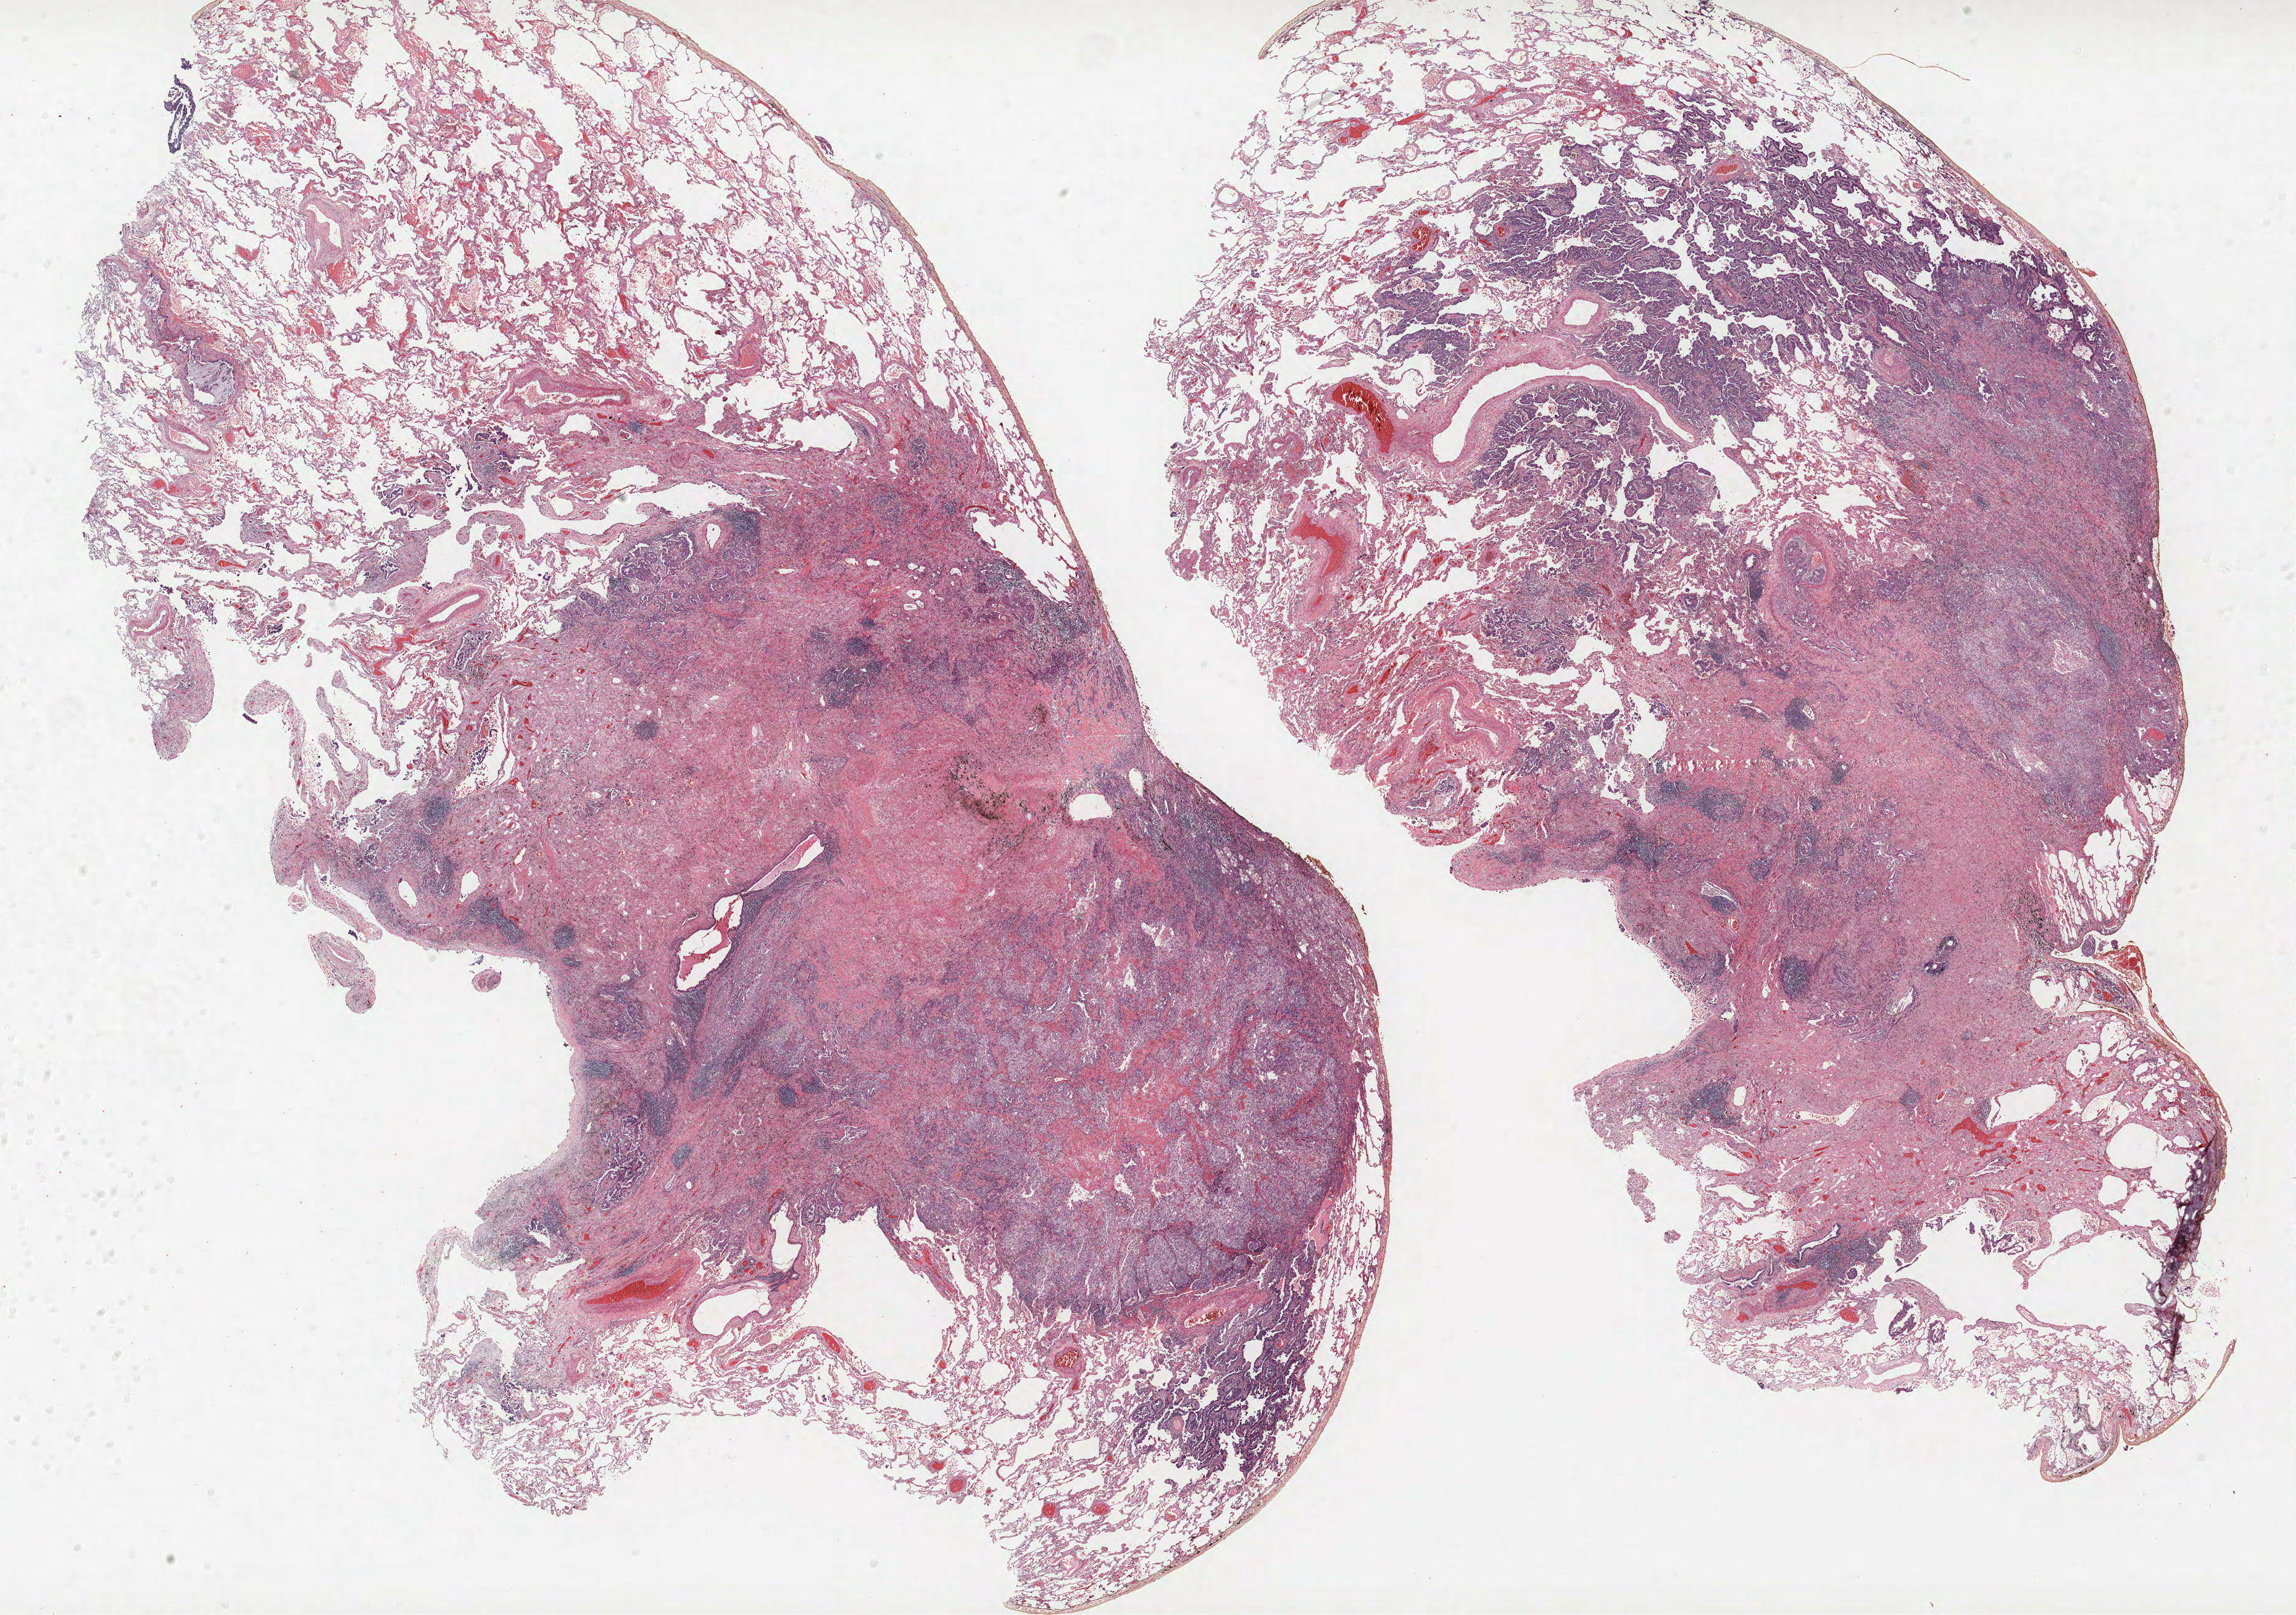
Whole-slide histology image, Hematoxylin and eosin (H&E) stained, whole scanned area (about 29.8 x 20.9 mm, from a 40x scan) shown as a low-resolution overview, FFPE section, lung. Male patient, aged 63 at enrolment. Grade: moderately differentiated (G2).
Stage (AJCC 6th edition): IA. Participant's lung-cancer diagnosis: Adenocarcinoma, NOS. Tumour size (pathology): 12 mm. Primary tumour location (clinical record): right lower lobe. Note: participant had 3 primary lung cancers recorded; fields above describe the first.